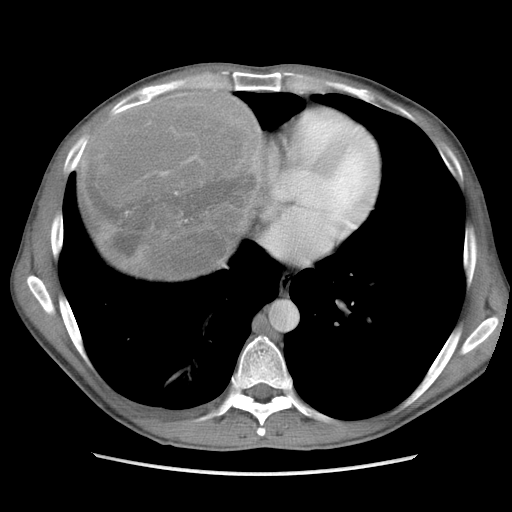
Contrast-enhanced abdominal CT, one axial slice. Slice 98 of 115 in the series (ordered by position). Soft-tissue window (W 400 / L 40 HU). 512 × 512 image matrix. Male patient. Case-level facts recorded for this patient, not image findings: diagnosis: adrenocortical carcinoma; tumour side: right adrenal; Ki-67 index: 13 %; stage (as recorded): 3.
Structures marked on this image (semi-automatically segmented with operator editing):
- mass: bounding box [x1, y1, x2, y2] px = [85, 91, 264, 278]